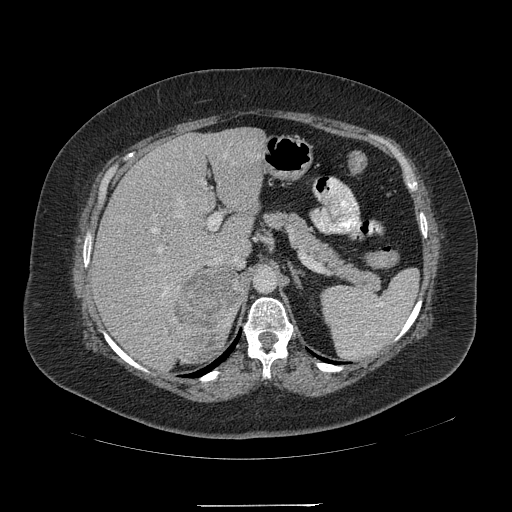
Contrast-enhanced abdominal CT, one axial slice. Slice 141 of 217 in the series (ordered by position). Reconstruction kernel STANDARD. Intravenous contrast given. Soft-tissue window (W 400 / L 40 HU). 1.25 mm slice thickness. 512 × 512 image matrix. Patient: female, 55 years. Case-level facts recorded for this patient, not image findings: diagnosis: adrenocortical carcinoma; tumour side: right adrenal; tumour size at pathology: 11 cm; Ki-67 index: 20 %; stage (as recorded): 2.
Annotated regions visible in this slice (semi-automatically segmented with operator editing):
- mass: bounding box <169,268,240,361> (left, top, right, bottom; pixels)